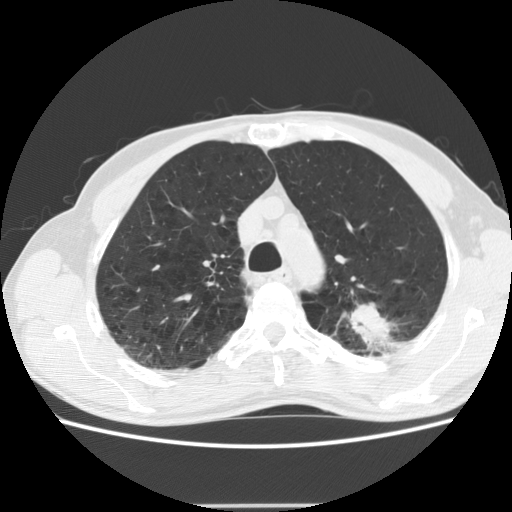
Axial slice from a low-dose chest CT screening exam, first (baseline) screen, lung window (W 1500 / L -600 HU), standard (soft-tissue) reconstruction kernel (STANDARD), slice 46 of 191 in the series. Male participant, aged 64 years at enrolment. Current smoker at enrolment.
Lesion marked by an expert reader, bounding box (x1, y1, x2, y2) in pixels: (340, 284, 435, 359). Screening reader's record for this exam (one nodule recorded; not confirmed to be the boxed lesion): non-calcified nodule or mass ≥4 mm, left upper lobe, 27 × 19 mm, poorly defined margins, soft tissue attenuation. Official screen result: positive, change unspecified: nodule(s) >= 4 mm or enlarging nodule(s), mass(es), or other non-specific abnormalities suspicious for lung cancer. Later outcome: lung cancer diagnosed 23 days after this screen — adenocarcinoma, NOS, left upper lobe, moderately differentiated (G2), stage IA (AJCC 6th edition), 29 mm at pathology.